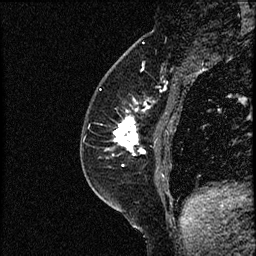
Breast MRI (dynamic contrast-enhanced), one sagittal slice. Slice 23 of 52 in the series (ordered by position). Dynamic contrast-enhanced study with each time point stored as its own series, time point 2 of 3 at this slice position (early post-contrast, ordered by acquisition time). 1.5 T. TE 4.2 ms, TR 17.6 ms. 256 × 256 image matrix, field of view 200 × 200 mm. Patient: female, 49 years. Case-level facts recorded for this patient, not image findings: setting: breast cancer imaged before/during neoadjuvant chemotherapy; receptor status: HER2-positive.
Annotated regions visible in this slice (semi-automatic segmentation, software-assisted and operator-edited):
- analysis volume of interest (the breast-tissue region the enhancement analysis was run in; not a lesion): bounding box (x1, y1, x2, y2) in pixels: (85, 65, 182, 175)
- tumour enhancement mask (voxels above the 100 % enhancement threshold inside the analysis volume of interest): (114, 99, 149, 155)